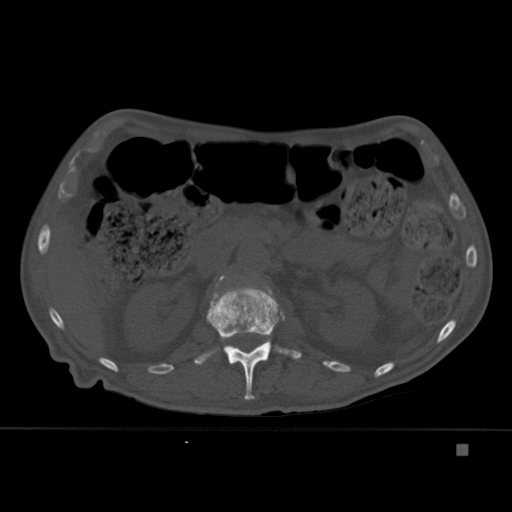
CT including the spine, one axial slice. Slice 179 of 451 in the series (ordered by position). Bone window (W 1800 / L 400 HU). 512 × 512 image matrix, field of view 378 × 378 mm. Patient: male, 75 years. From the clinical record (not read from this slice): primary cancer: prostate.
Annotated regions visible in this slice (semi-automatic segmentation, software-assisted and operator-edited):
- L1 vertebra: bounding box <194,284,301,400> (left, top, right, bottom; pixels)
- L2 vertebra: <219,275,226,281>